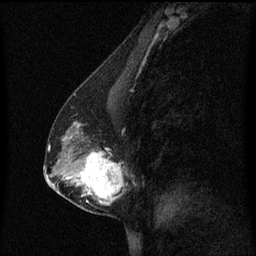
Breast MRI (dynamic contrast-enhanced), one sagittal slice. Position 31 of 60 along the scan axis. Dynamic contrast-enhanced series, image 2 of 3 at this slice position (ordered by acquisition). 1.5 T. TE 4.2 ms, TR 8.4 ms. 2 mm slice thickness. 256 × 256 image matrix, field of view 200 × 200 mm. Female patient, age 40 years. From the clinical record (not read from this slice): setting: breast cancer imaged before/during neoadjuvant chemotherapy; receptor status: triple-negative.
Annotated regions visible in this slice (semi-automatic segmentation, software-assisted and operator-edited):
- analysis volume of interest (the breast-tissue region the enhancement analysis was run in; not a lesion): bounding box (x1, y1, x2, y2) in pixels: (60, 122, 131, 215)
- tumour enhancement mask (voxels above the 70 % enhancement threshold inside the analysis volume of interest): (64, 122, 123, 205)